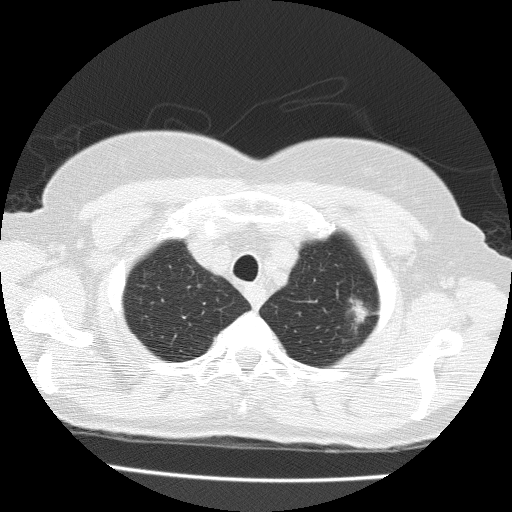
Chest CT (low-dose screening protocol), one axial image, baseline screening round, lung window (W 1500 / L -600 HU), 2 mm slice thickness, lung (sharp) reconstruction kernel (FC51), 512 × 512 image matrix. Female, age 71 years at enrolment. Former smoker at enrolment.
- Expert reader's lesion annotation, bounding box (x1, y1, x2, y2) in pixels: (339, 292, 388, 335).
- The exam's reader record, not a measurement of the box and not confirmed to be the same lesion: non-calcified nodule or mass ≥4 mm, left upper lobe, 15 × 10 mm, spiculated (stellate) margins, soft tissue attenuation.
- Official screen result: positive, change unspecified: nodule(s) >= 4 mm or enlarging nodule(s), mass(es), or other non-specific abnormalities suspicious for lung cancer.
- Later outcome: lung cancer diagnosed 49 days after this screen — adenocarcinoma with mixed subtypes, left upper lobe, well differentiated (G1), stage IA (AJCC 6th edition), 15 mm at pathology.